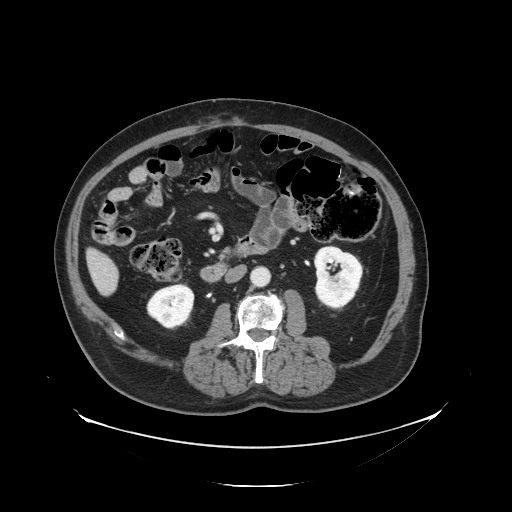
Contrast-enhanced abdominal CT, one axial slice. Position 37 of 138 along the scan axis. Reconstruction kernel STANDARD. 120 kVp. Intravenous contrast given. Soft-tissue window (W 400 / L 40 HU). 512 × 512 image matrix. Male patient, age 77 years. Case-level facts recorded for this patient, not image findings: diagnosis: colorectal cancer liver metastases, imaged before liver resection; multiple liver metastases: no; largest metastasis: 1.5 cm; chemotherapy before resection: no.
Structures marked on this image (outlined manually by an expert reader):
- liver: bounding box (x1, y1, x2, y2) in pixels: (89, 251, 119, 294)
- planned liver remnant (the part of the liver to remain after resection): (89, 251, 115, 275)